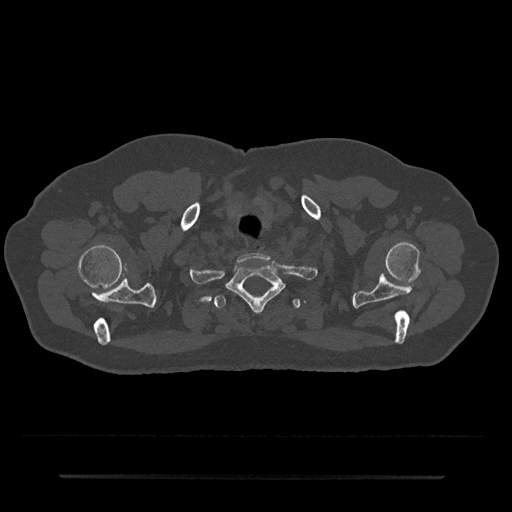
CT including the spine, one axial slice. Slice 637 of 797 in the series (ordered by position). Reconstruction kernel Br40s/3. 120 kVp. Bone window (W 1800 / L 400 HU). 512 × 512 image matrix, field of view 437 × 437 mm. Patient: male, 69 years. Case-level facts recorded for this patient, not image findings: primary cancer: prostate.
Annotated regions visible in this slice (semi-automatically segmented with operator editing):
- T1 vertebra: bounding box (x1, y1, x2, y2) in pixels: (227, 263, 284, 312)
- T2 vertebra: (214, 295, 301, 309)